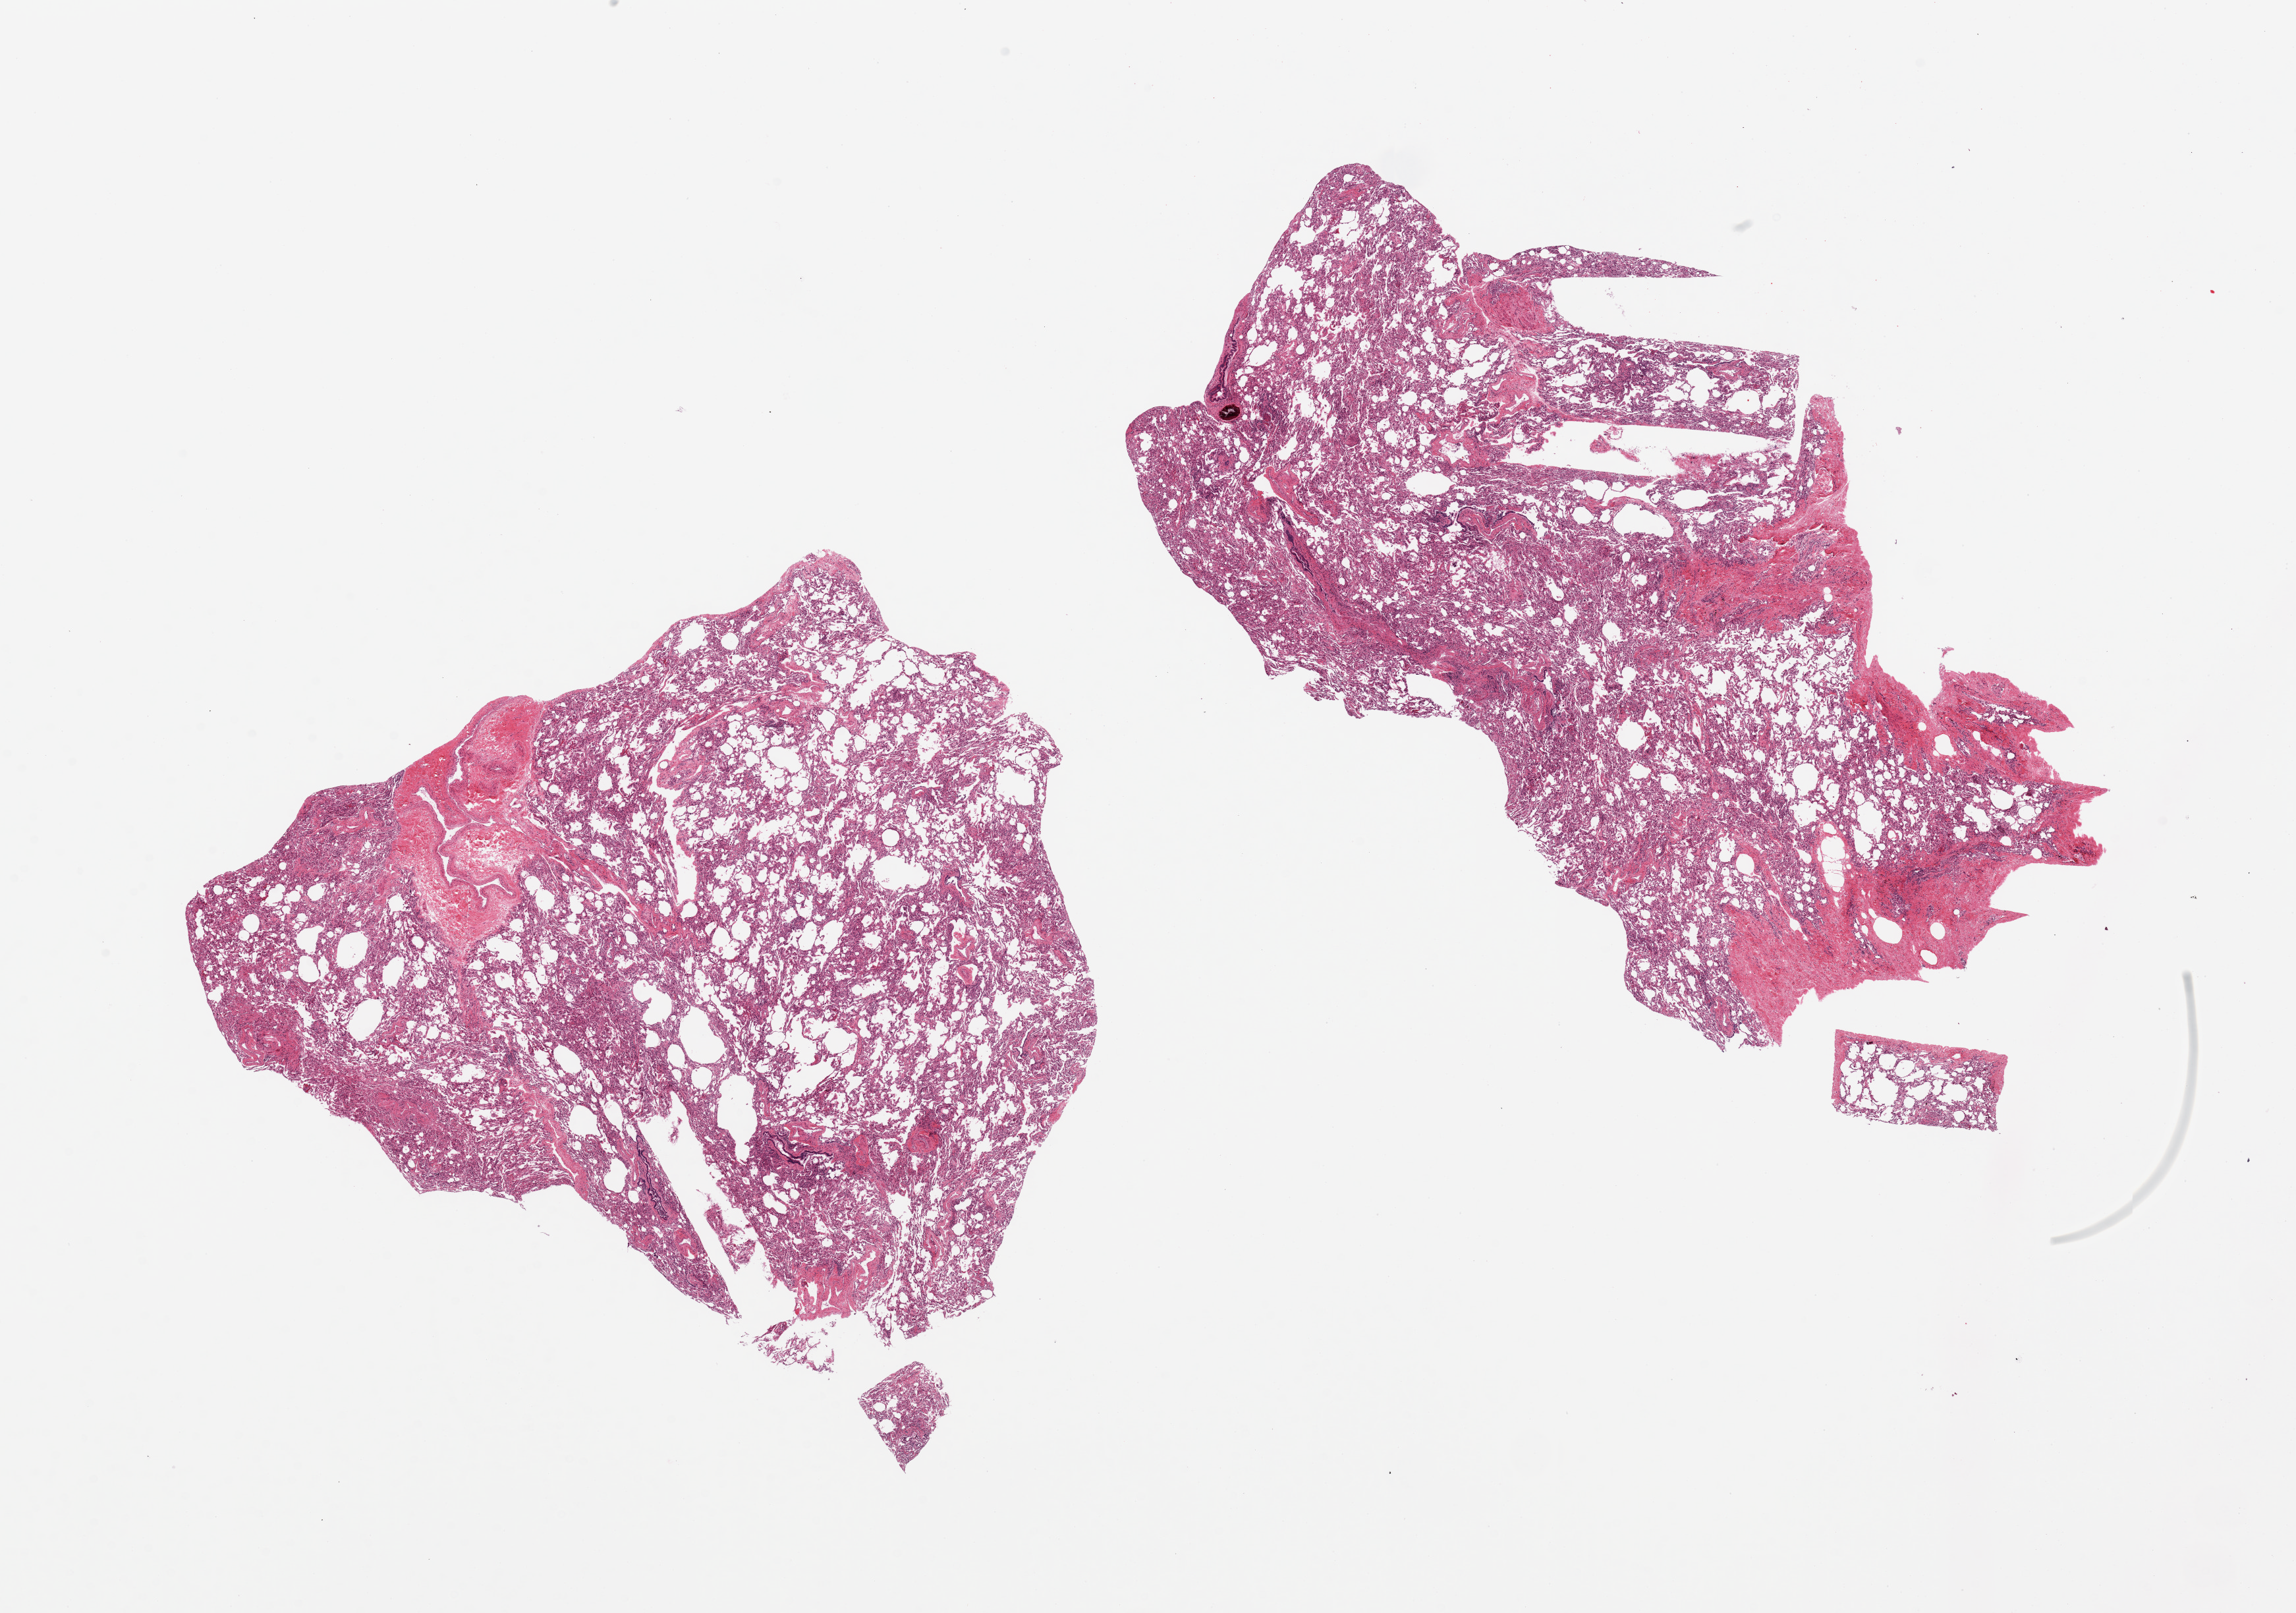
H&E whole-slide image — shown as a low-resolution overview of the whole scanned area (about 27.6 x 19.4 mm, acquisition: 20x scan), PAXgene-fixed, paraffin-embedded tissue, sampled site (target tissue): lung, donor tissue sample. Donor sex: female.
- review note (as recorded): 2 pieces, some atelectasis and interstitial fibrosis, pulmonary macrophages, focus of vascular calcification